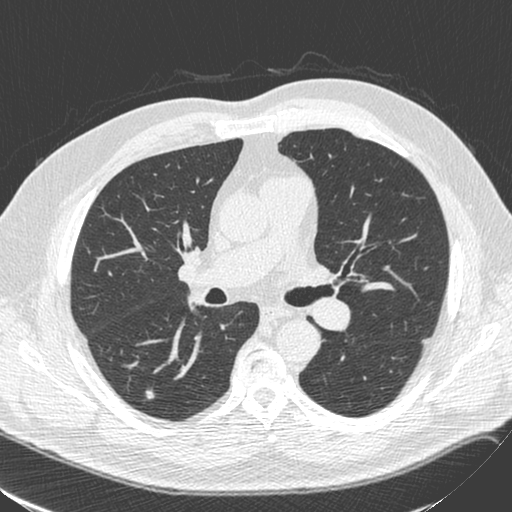
Low-dose screening chest CT, axial slice. Baseline annual screen. Lung window (W 1500 / L -600 HU). 1.3 mm slice thickness. Standard (soft-tissue) reconstruction kernel (C). Slice 98 of 248 in the series. 512 × 512 image matrix. Male, age 71 years at enrolment. Former smoker at enrolment.
Expert-annotated lung lesion, bounding box <135,381,167,409> (left, top, right, bottom; pixels). The exam's reader record, not a measurement of the box and not confirmed to be the same lesion: non-calcified nodule or mass ≥4 mm, right lower lobe, 6 × 6 mm, smooth margins, soft tissue attenuation. Official screen result: positive, change unspecified: nodule(s) >= 4 mm or enlarging nodule(s), mass(es), or other non-specific abnormalities suspicious for lung cancer. Later outcome: lung cancer diagnosed 231 days after this screen — squamous cell carcinoma, NOS, right lower lobe, poorly differentiated (G3), stage IA (AJCC 6th edition), 4 mm at pathology.